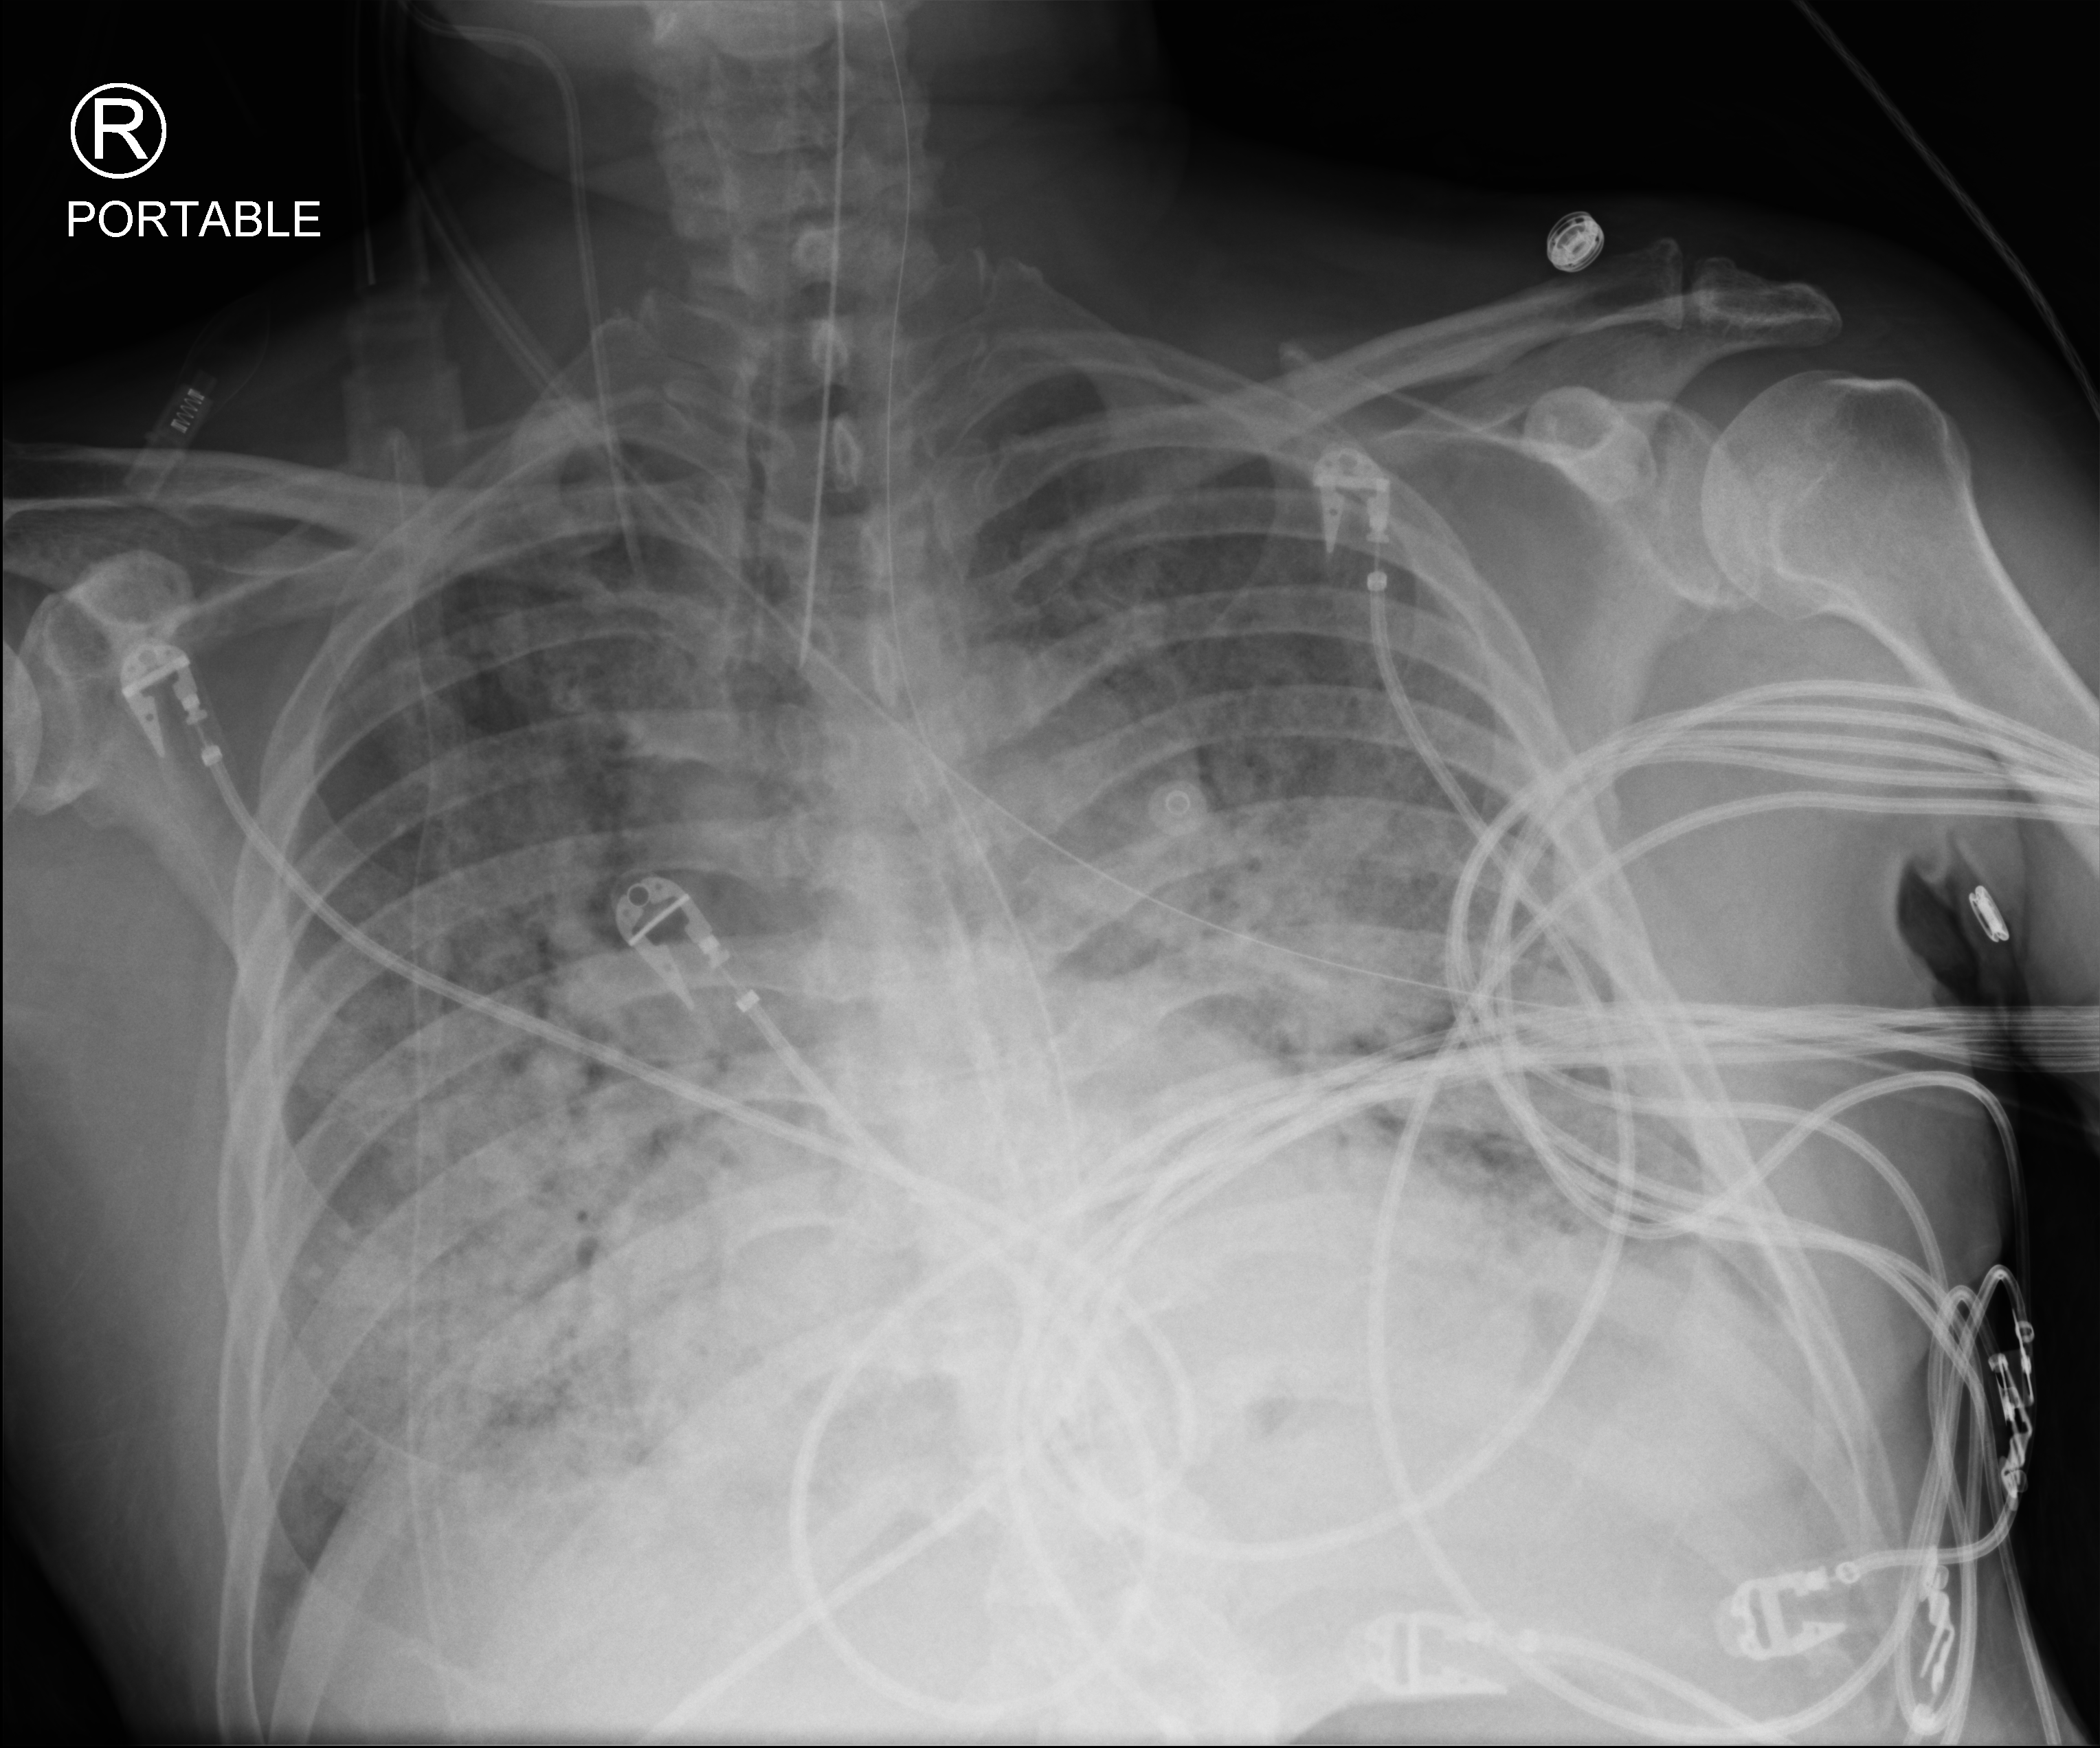
Portable chest radiograph; anteroposterior (AP) projection. Patient hospitalised with COVID-19; male, aged 60–74 years.
Hospital-stay facts (about this admission, not read from this image; timing relative to this image not recorded):
- admitted to intensive care during this hospital stay: yes
- hypertension (admission record): yes
- length of hospital stay: 28 days